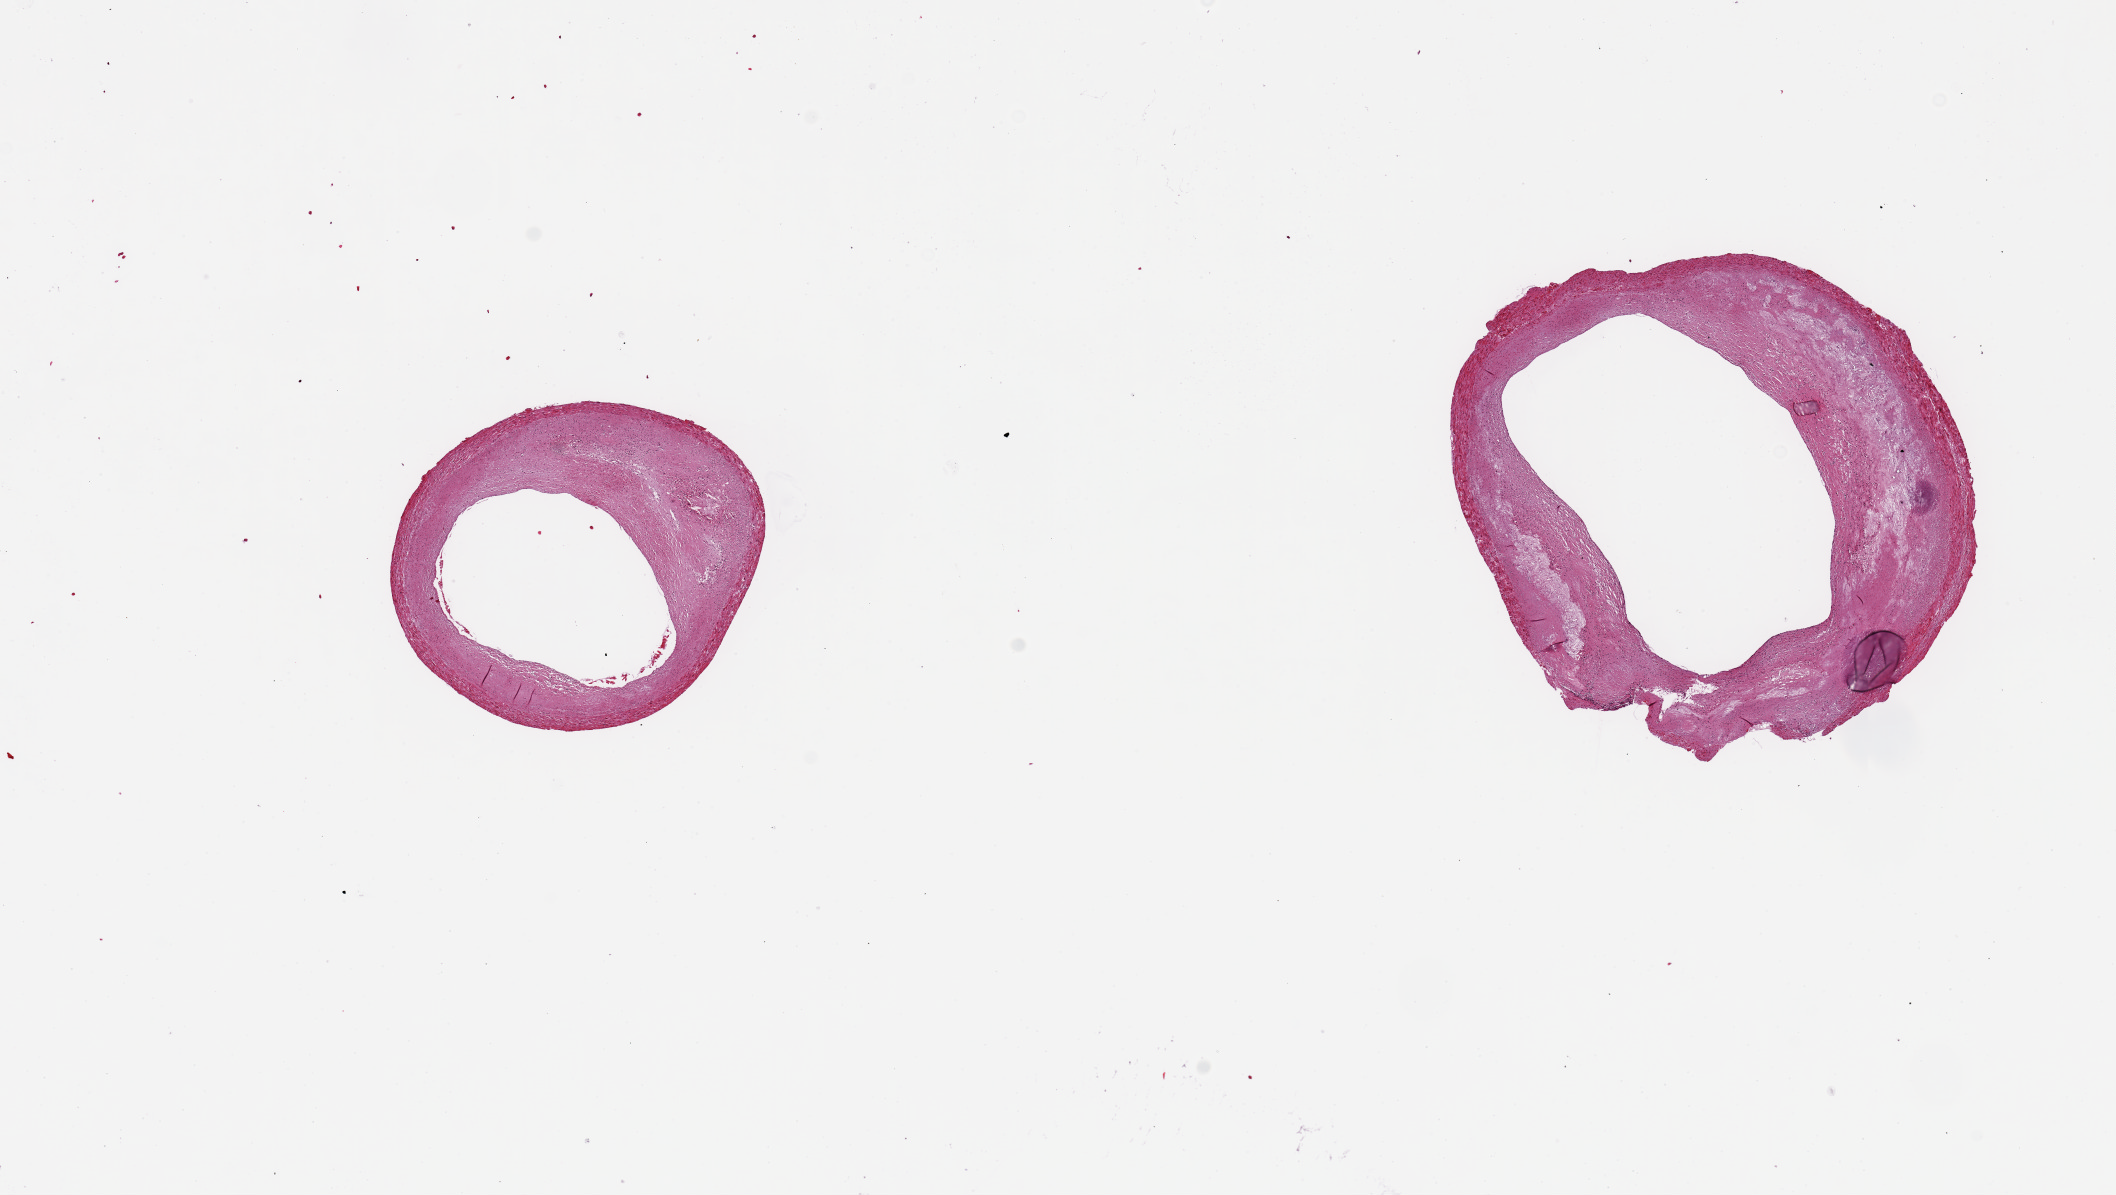
Digitized haematoxylin and eosin-stained section, brightfield, whole scanned area (about 16.7 x 9.5 mm, from a 20x scan) shown as a low-resolution overview, PAXgene-fixed paraffin-embedded (PFPE) section, sampled site (target tissue): coronary artery, donor tissue sample. Donor: male.
Pathologist's review note for this sample: 2 pieces, 3x2.5 & 4x4mm; ave d. ~3mm, up to ~50% occlusive atheroscerotic deposits.